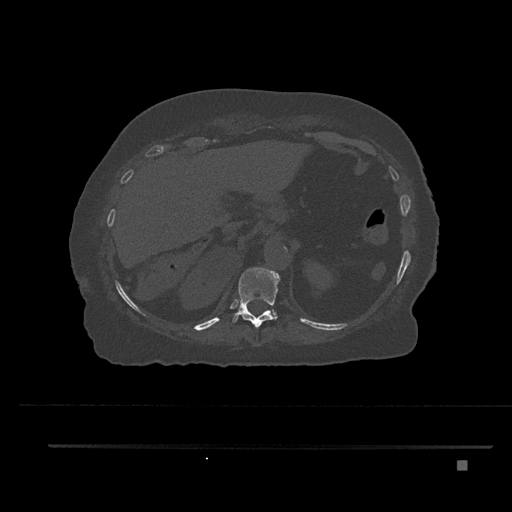
CT including the spine, one axial slice. Position 310 of 797 along the scan axis. Reconstruction kernel Br40s/3. Bone window (W 1800 / L 400 HU). 0.5 mm slice thickness. 512 × 512 image matrix, field of view 437 × 437 mm. Patient: female, 76 years. Case-level facts recorded for this patient, not image findings: primary cancer: lung.
Structures marked on this image (semi-automatic segmentation, software-assisted and operator-edited):
- T11 vertebra: bounding box <231,267,280,328> (left, top, right, bottom; pixels)